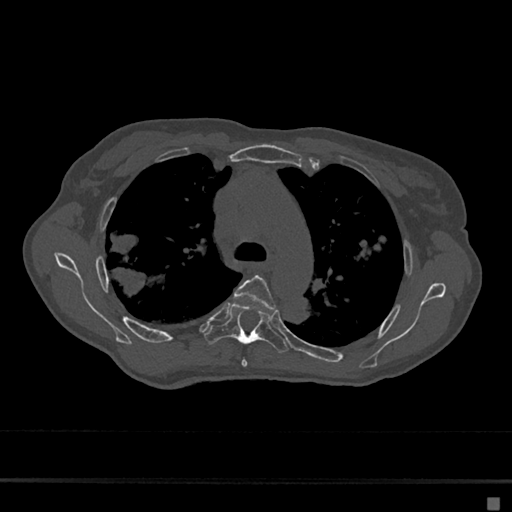
CT including the spine, one axial slice. Position 476 of 797 along the scan axis. Reconstruction kernel Br40s/3. Bone window (W 1800 / L 400 HU). 0.5 mm slice thickness. 512 × 512 image matrix. Patient: female, 68 years. From the clinical record (not read from this slice): primary cancer: renal.
Outlined on this slice (semi-automatically segmented with operator editing):
- T4 vertebra: box from (x=235, y=275) to (x=276, y=367) px
- T5 vertebra: (x=205, y=303)–(x=289, y=353)